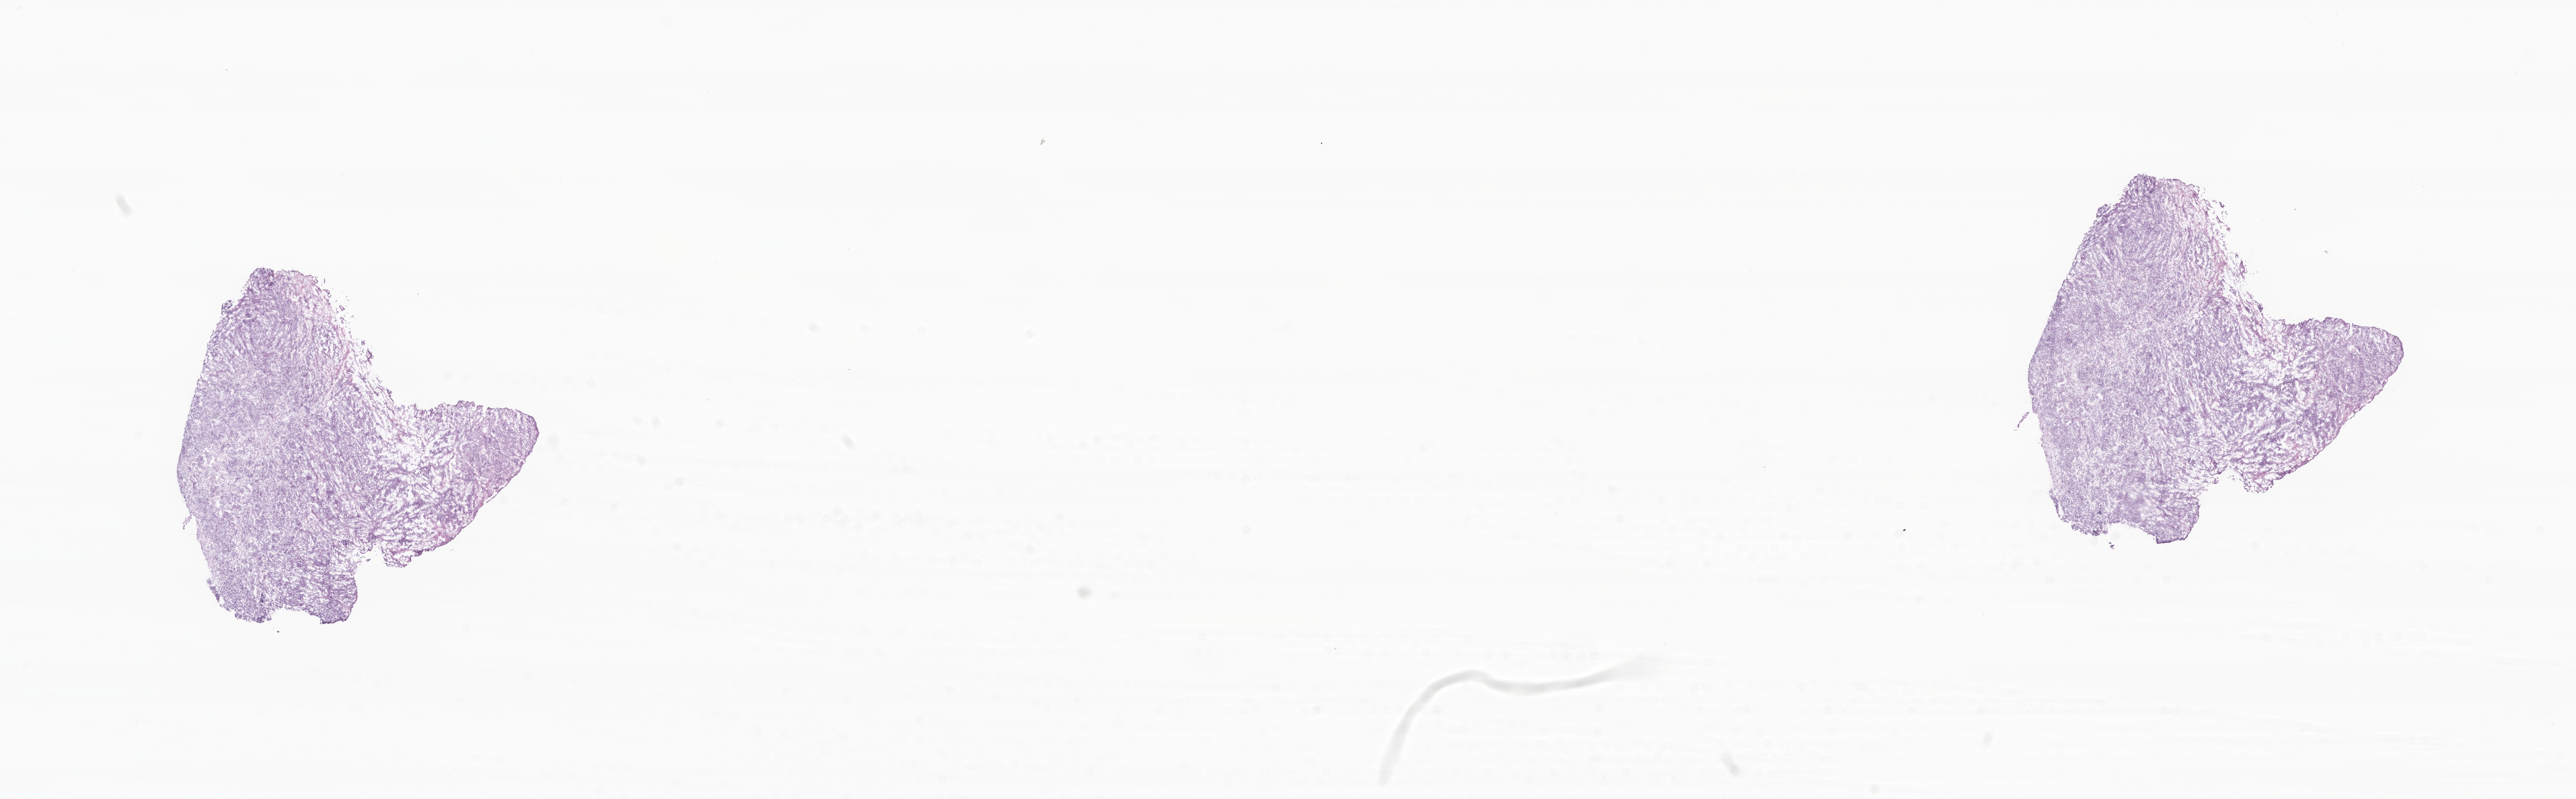
Digitized hematoxylin and eosin (H&E)-stained section, whole scanned area (about 27.7 x 8.6 mm) shown as a low-resolution overview. Cryosection. Metastatic tumor tissue. Female patient; age at initial diagnosis 54 years. Composition of this section per pathologist review: tumor cells 90%, tumor nuclei 90%, stromal cells 10%, necrosis 0%, normal cells 0%. Inflammatory infiltration, as recorded: lymphocyte infiltration 0%, monocyte infiltration 0%, neutrophil infiltration 0%.
Patient diagnosis (primary): Infiltrating duct carcinoma, NOS.